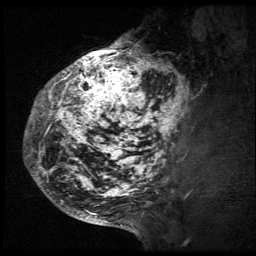
Breast MRI (dynamic contrast-enhanced), one sagittal slice. Slice 19 of 64 in the series (ordered by position). 3 images stored at this slice position (order not interpretable as contrast timing). 1.5 T. TE 4.2 ms, TR 9 ms. 256 × 256 image matrix. Female patient, age 50 years. From the clinical record (not read from this slice): setting: breast cancer imaged before/during neoadjuvant chemotherapy; receptor status: triple-negative.
Annotated regions visible in this slice (semi-automatically segmented with operator editing):
- analysis volume of interest (the breast-tissue region the enhancement analysis was run in; not a lesion): bounding box (x1, y1, x2, y2) in pixels: (24, 39, 194, 212)
- tumour enhancement mask (voxels above the 140 % enhancement threshold inside the analysis volume of interest): (25, 39, 191, 212)